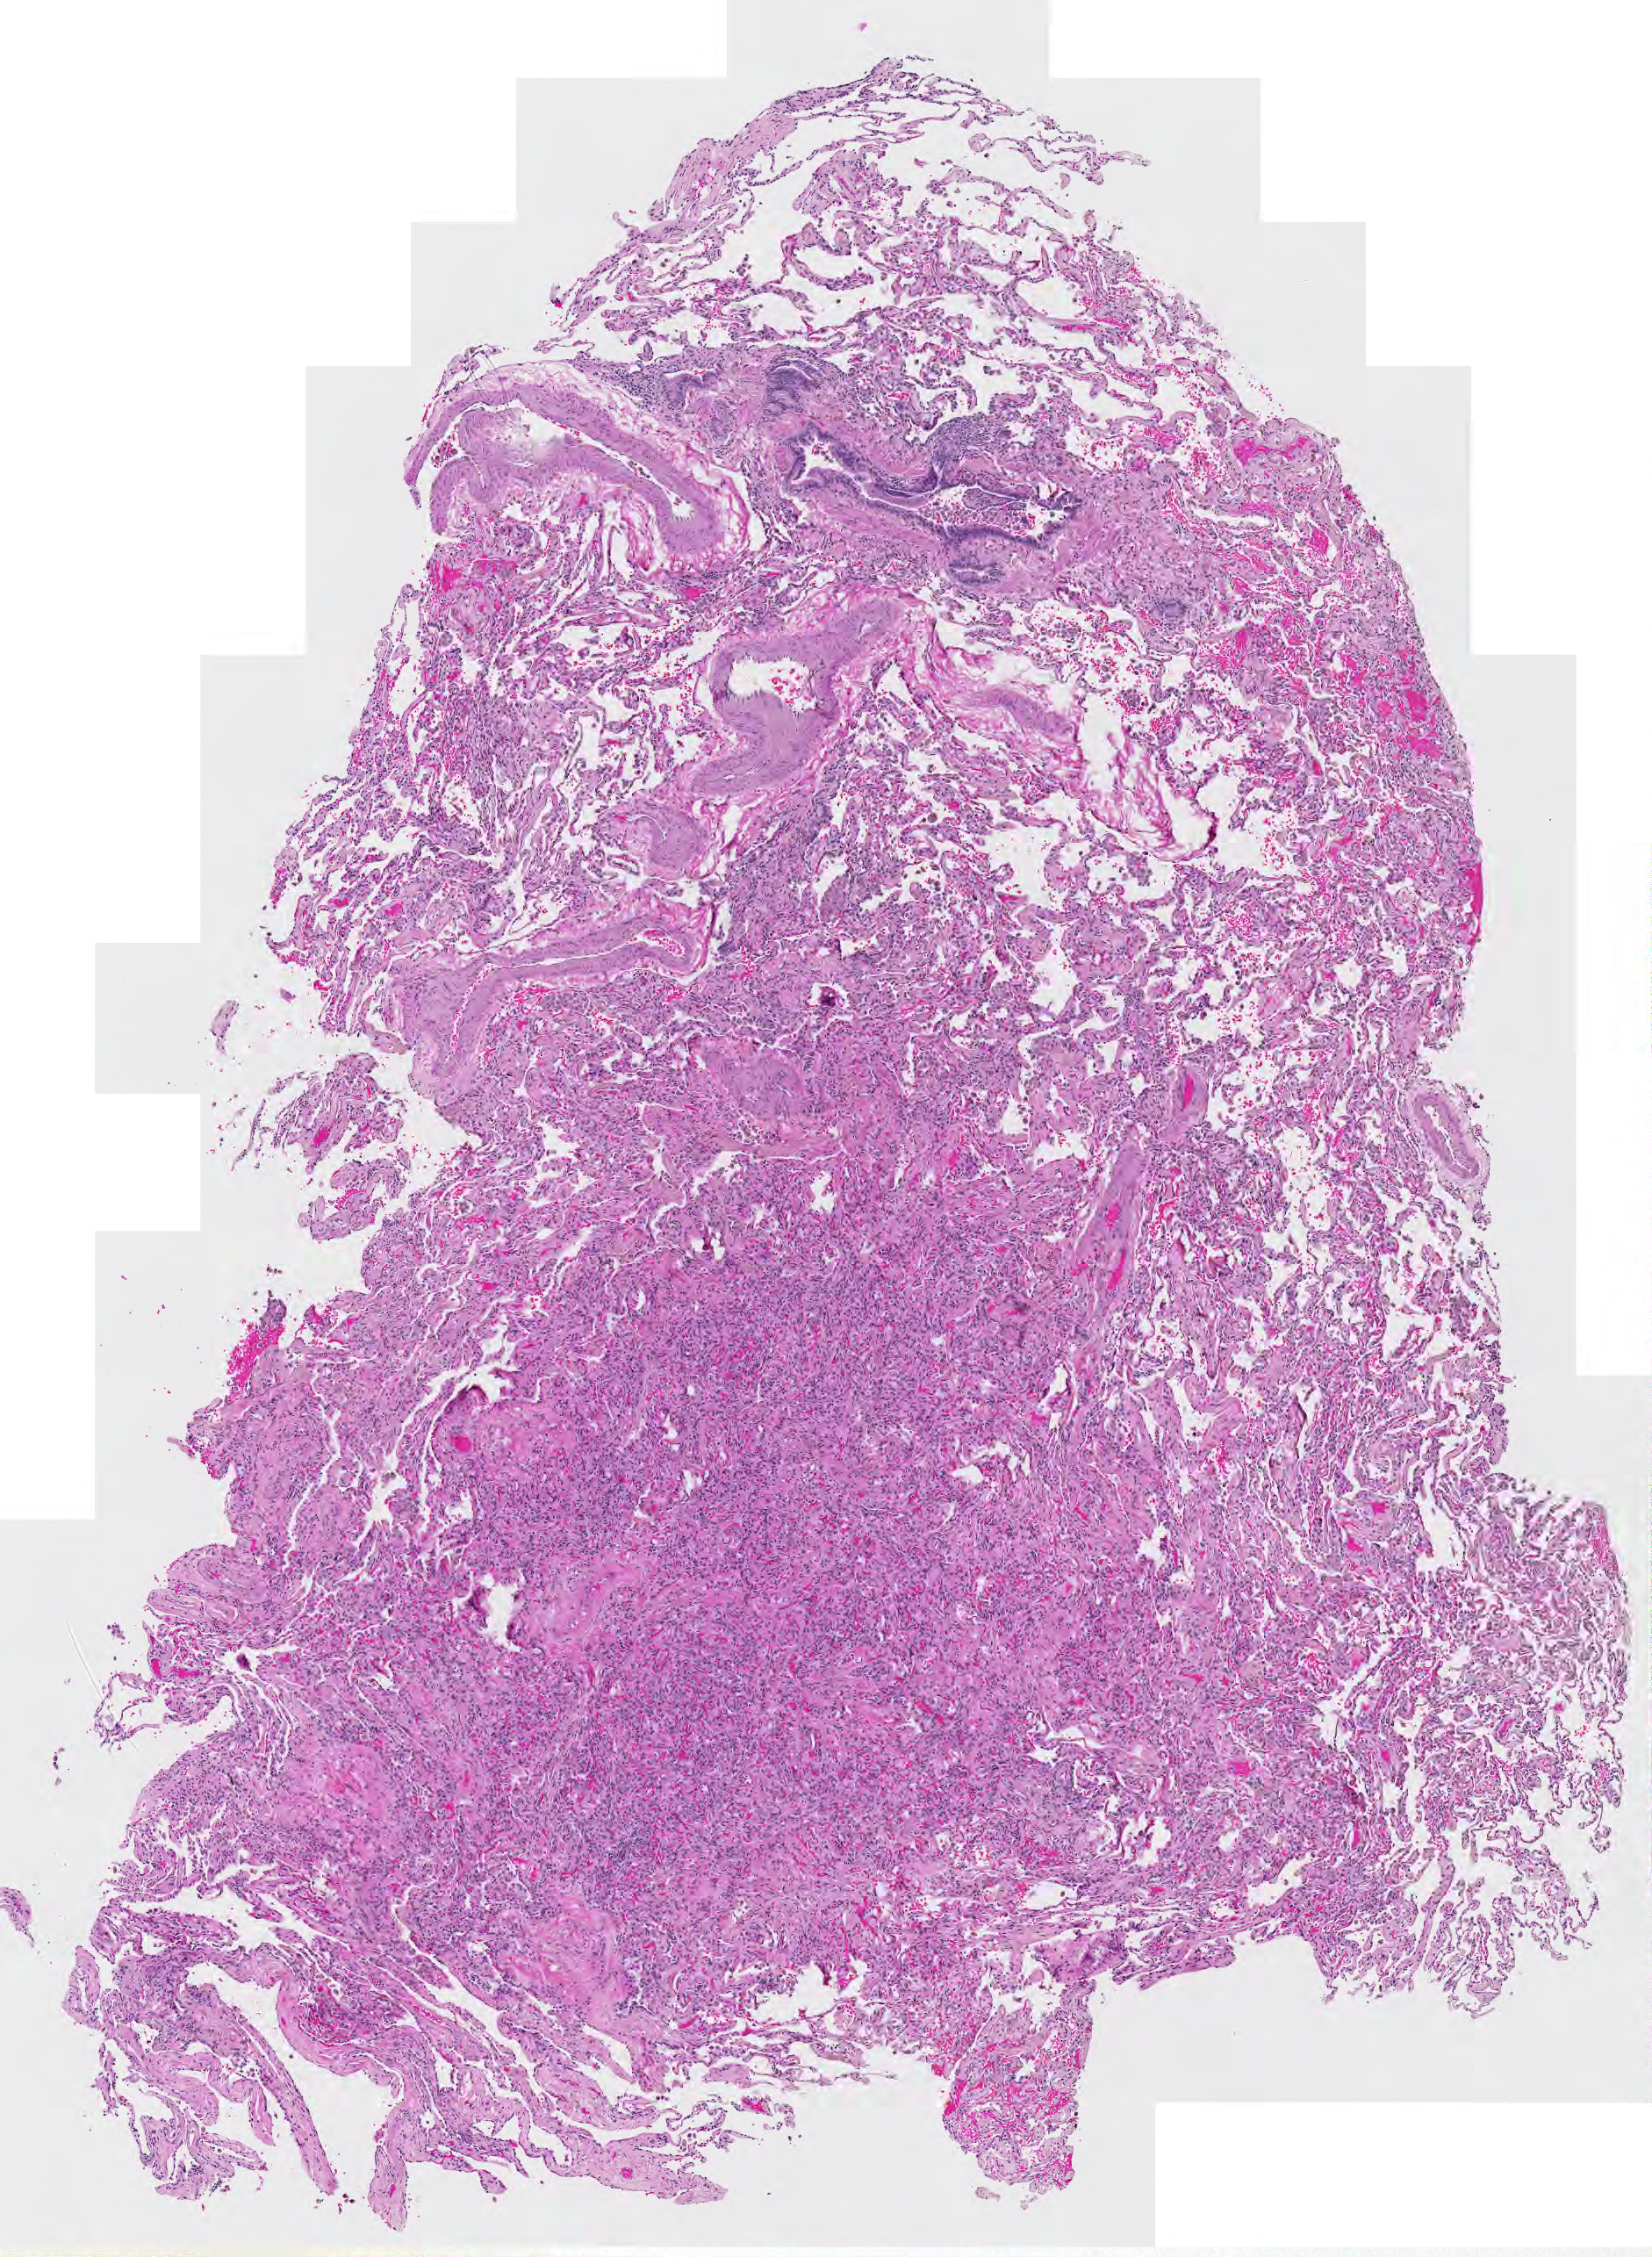
Digitized Hematoxylin and eosin (H&E) stained tissue section (whole slide), low-resolution overview of the scanned area, about 4.9 x 6.6 mm. Lung, normal (non-tumour) tissue. 68-year-old female patient.
This section: normal (non-tumour) tissue from the same patient. Patient diagnosis: Adenocarcinoma, NOS.